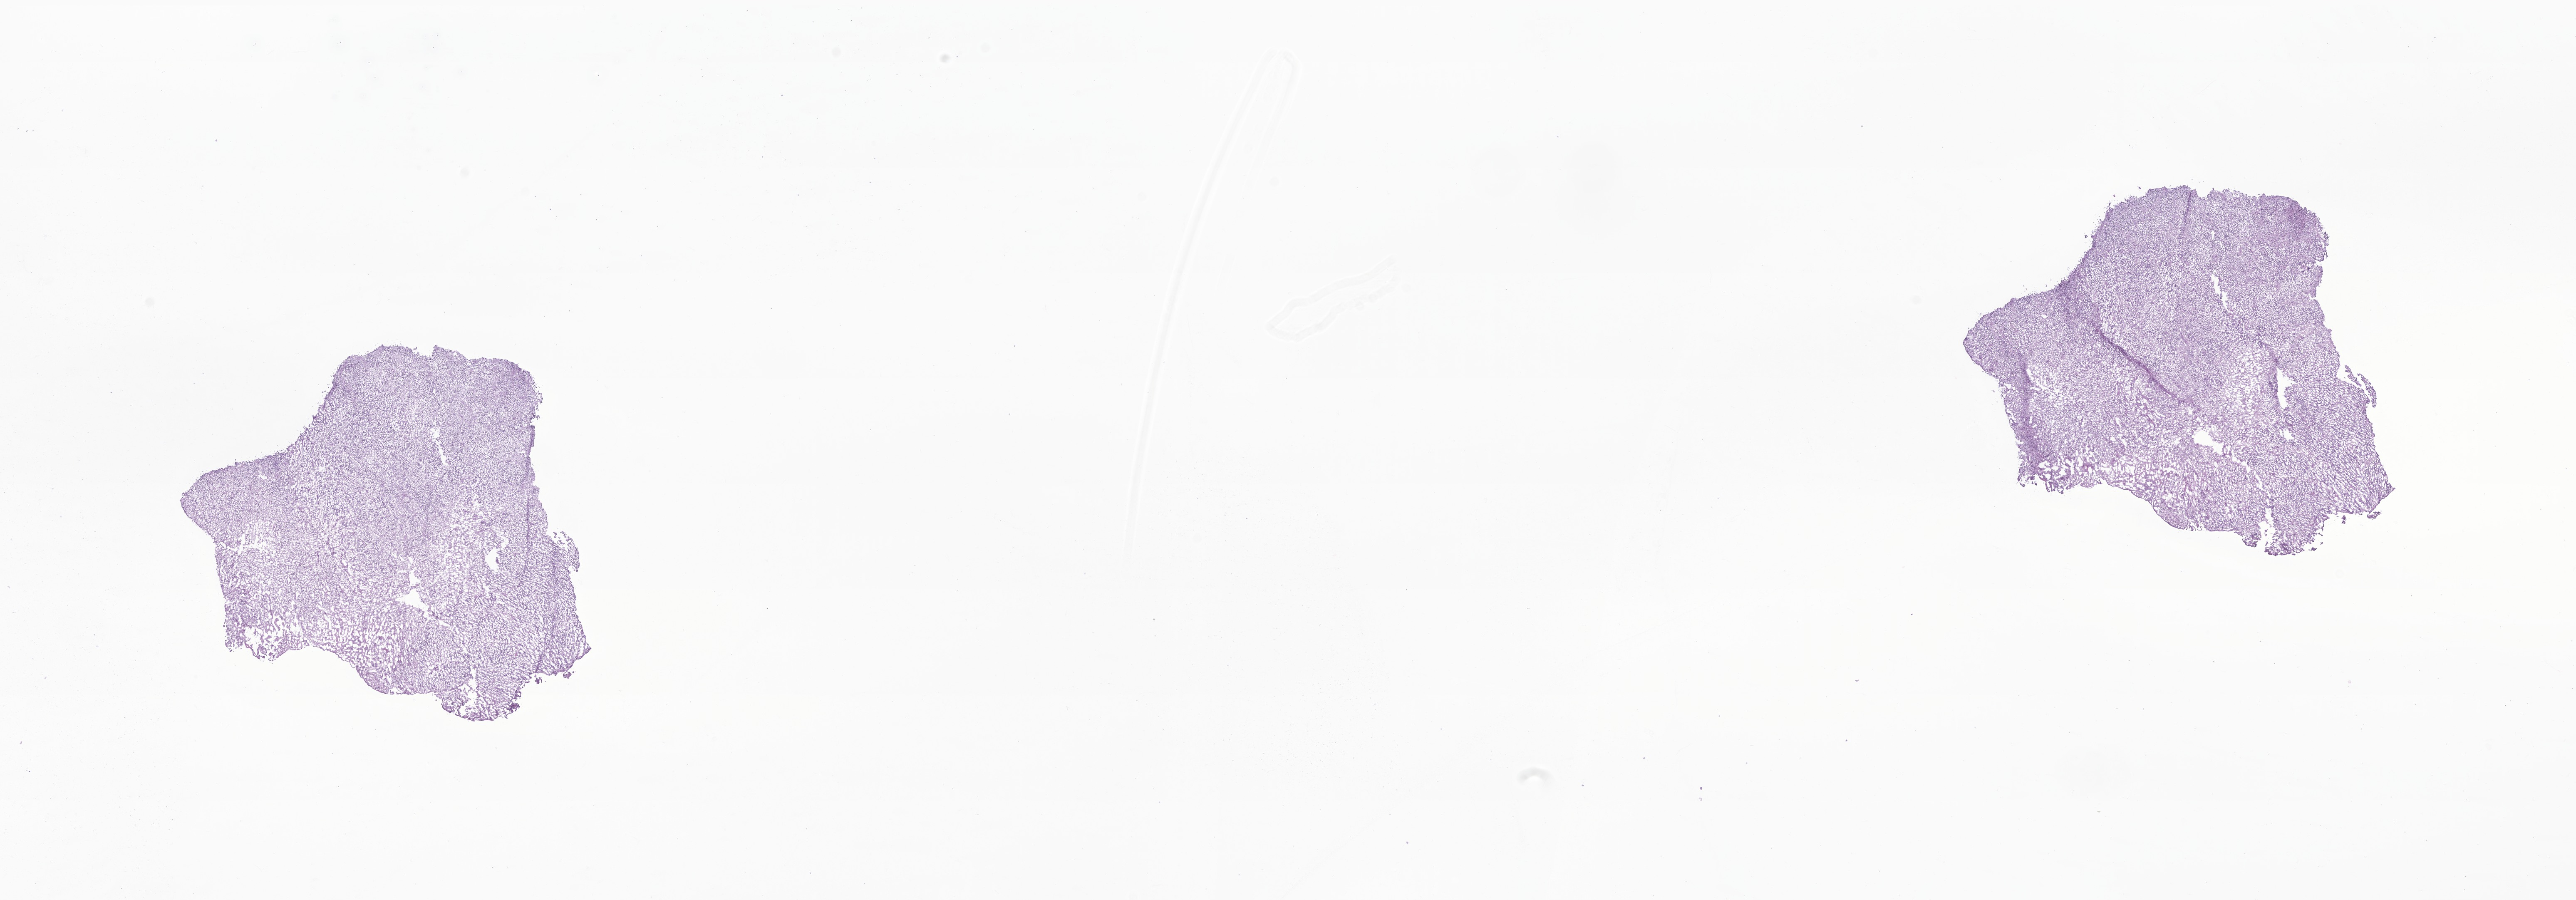
Whole-slide image, haematoxylin and eosin stain of tumor tissue from the cerebrum — low-resolution overview of the scanned area, about 26.1 x 9.1 mm, frozen section. Patient female; age 191 months (15 years 11 months).
- diagnosis: Ependymoma, NOS